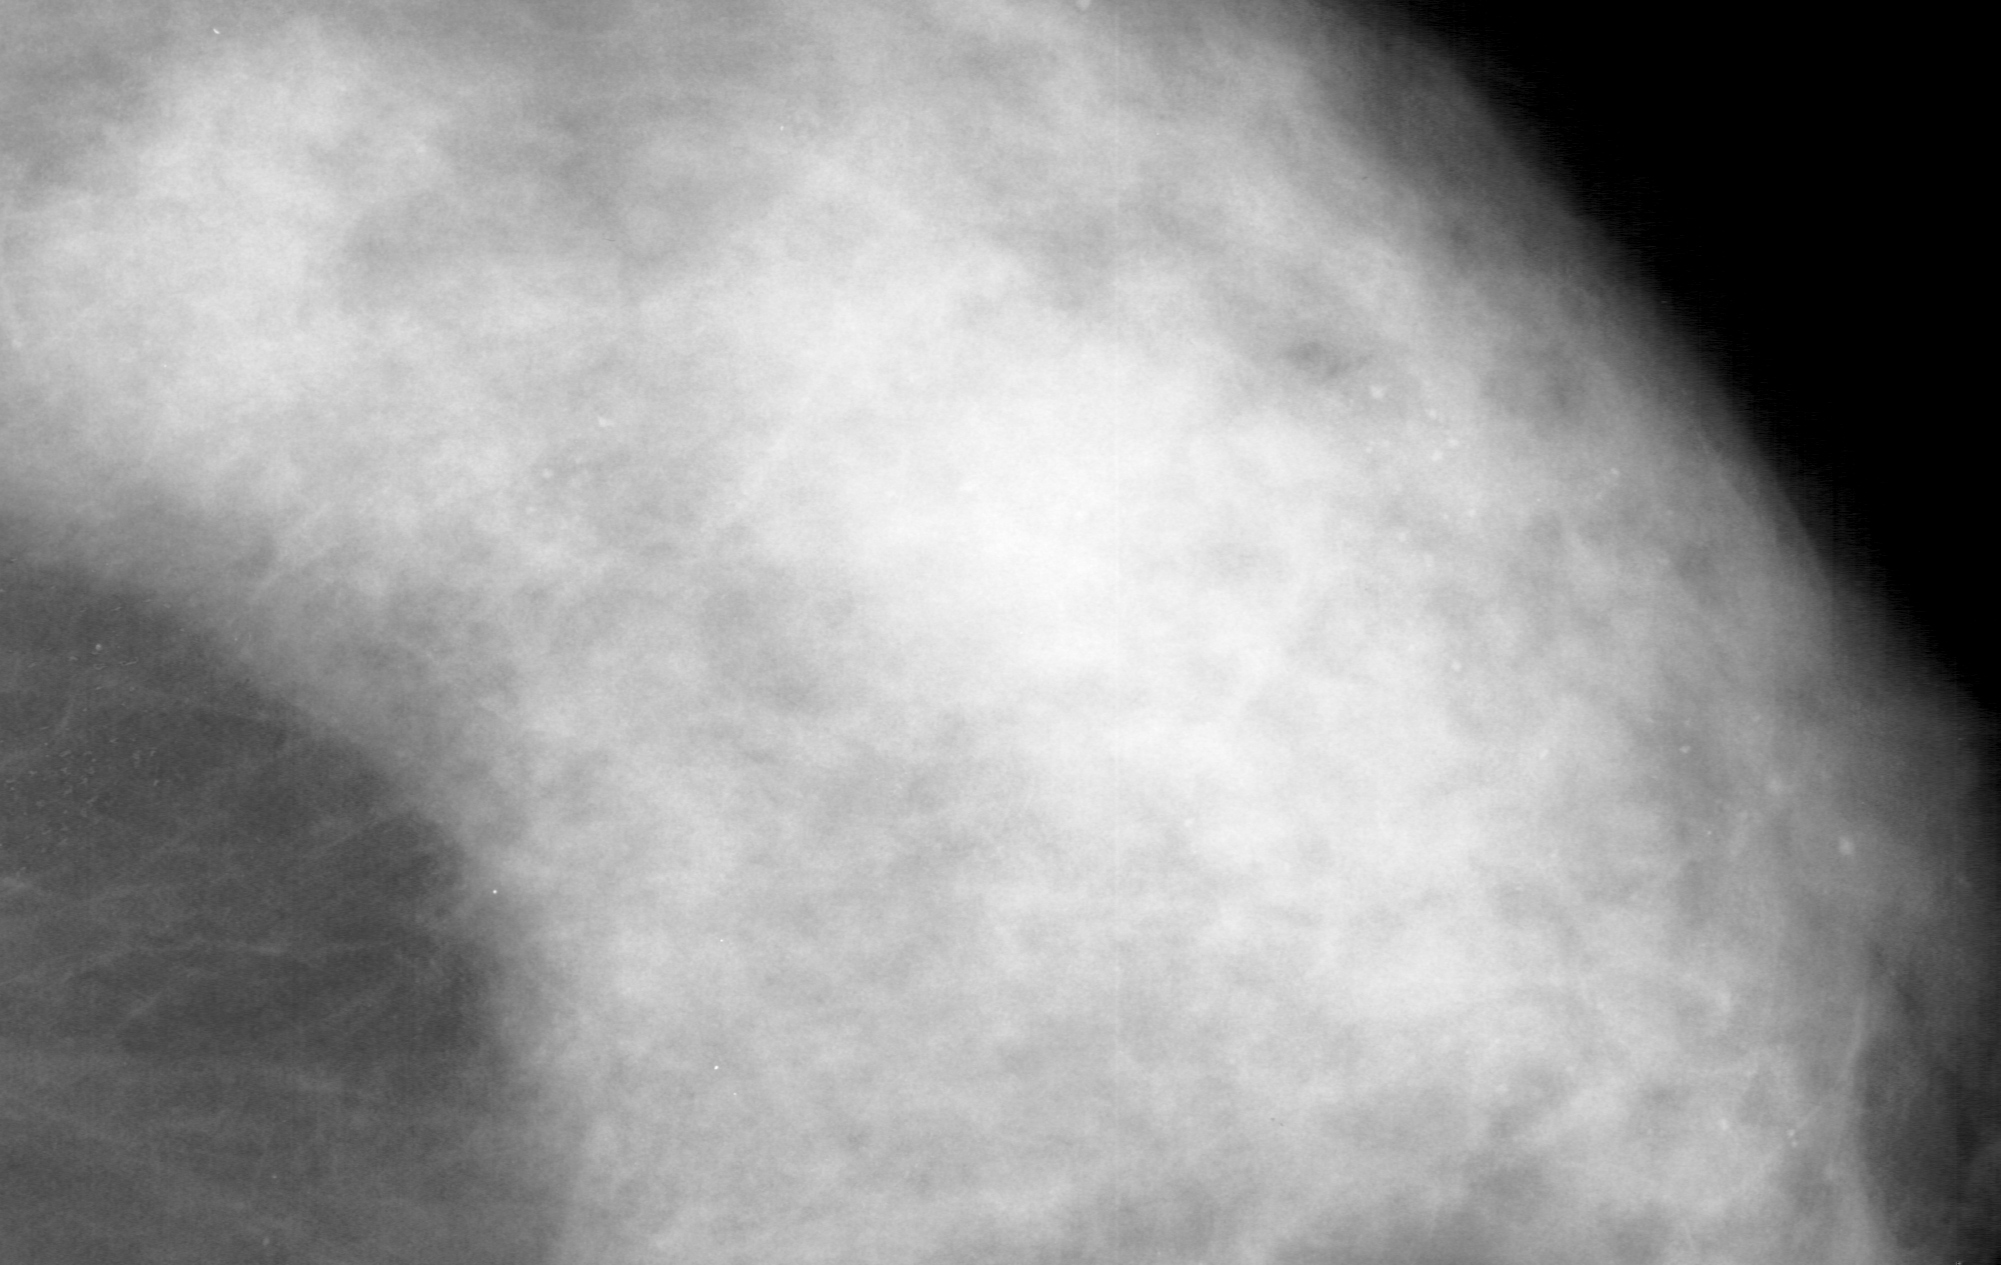
Cropped region of a digitized screen-film mammogram centred on a radiologist-marked abnormality; right breast; CC view; BI-RADS breast density category 4 (scale 1–4).
Finding: calcifications, morphology amorphous, distribution segmental; BI-RADS assessment category 4; subtlety rating 3 on a 1 (subtle) to 5 (obvious) scale; pathology (as recorded): benign.